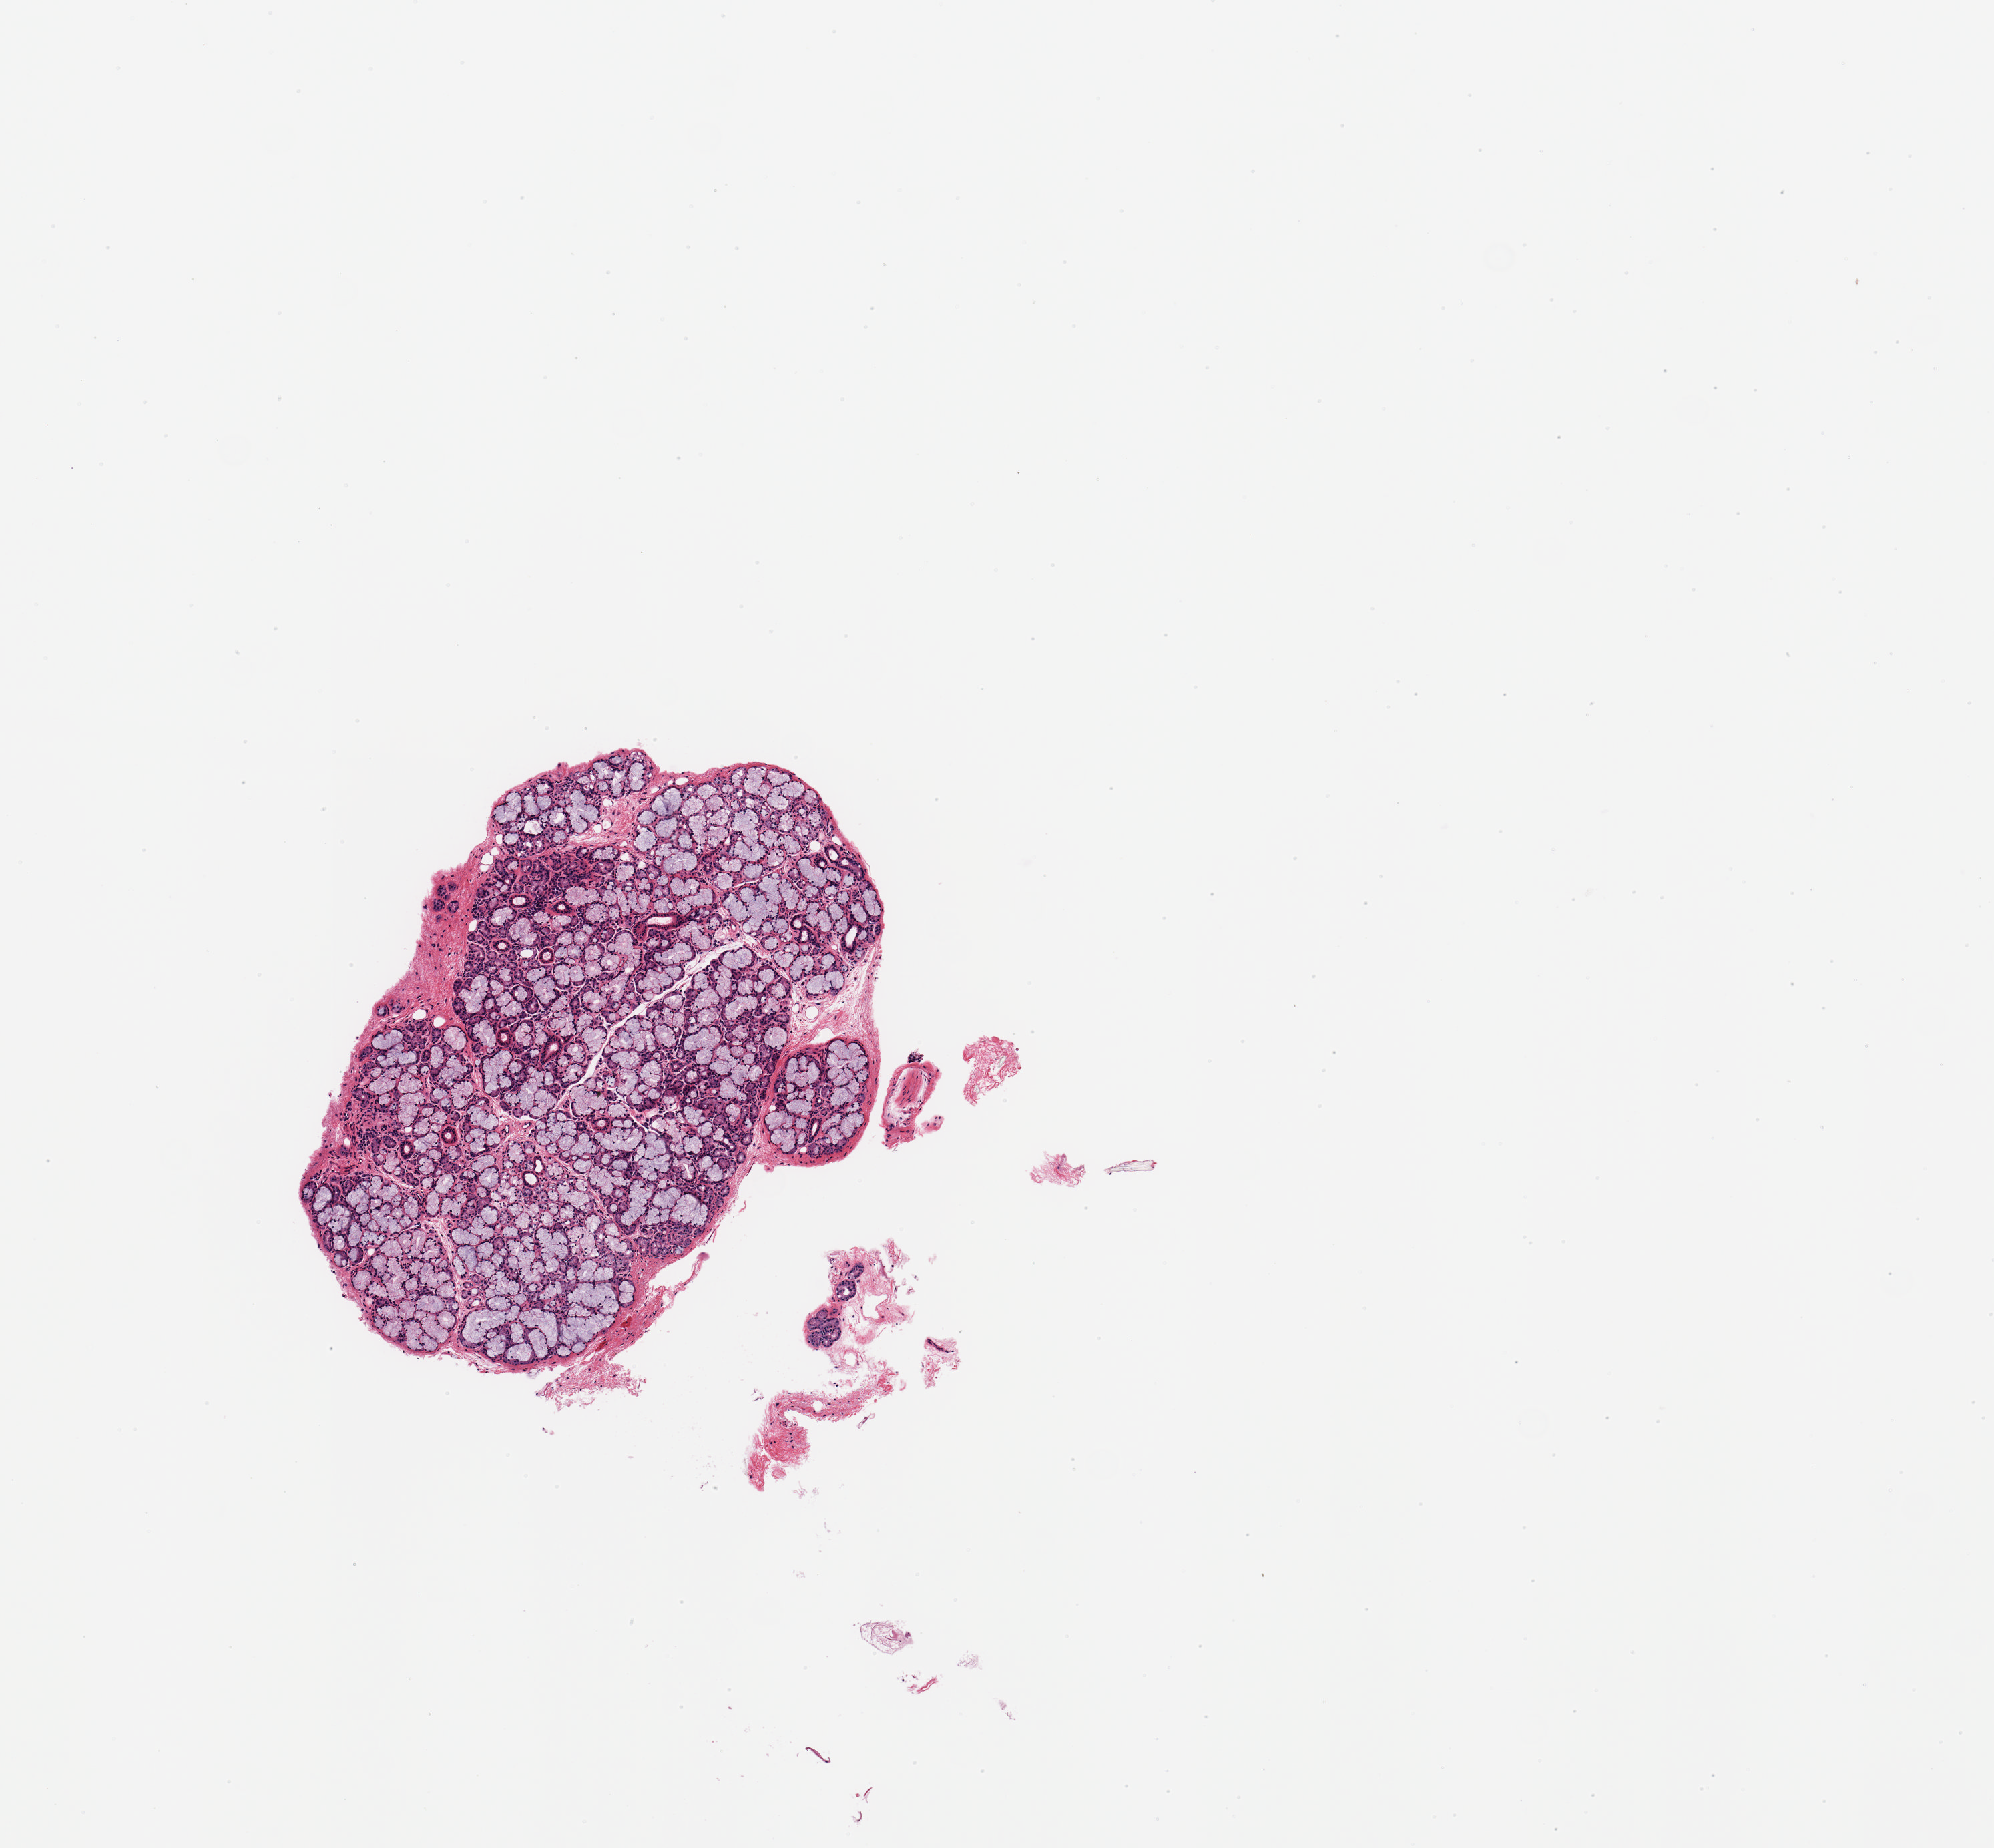
Whole-slide image, haematoxylin and eosin stain — low-resolution overview of the scanned area, about 5.9 x 5.5 mm, PAXgene-fixed, paraffin-embedded tissue, section of minor salivary gland (target tissue), tissue donor sample. Female donor.
* reviewer comment on this tissue sample: 1 piece, ~95% parenchyma